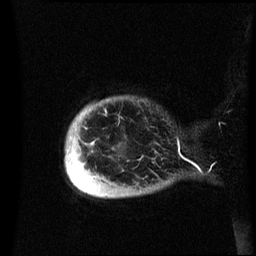
Breast MRI (dynamic contrast-enhanced), one sagittal slice. Position 3 of 60 along the scan axis. Dynamic contrast-enhanced series, image 2 of 3 at this slice position (ordered by acquisition). 1.5 T. TE 4.2 ms, TR 8.4 ms. 2.4 mm slice thickness. 256 × 256 image matrix, field of view 230 × 230 mm. Patient: female, 49 years.
Outlined on this slice (semi-automatic segmentation, software-assisted and operator-edited):
- analysis volume of interest (the breast-tissue region the enhancement analysis was run in; not a lesion): bounding box [x1, y1, x2, y2] px = [65, 97, 172, 198]
- tumour enhancement mask (voxels above the 70 % enhancement threshold inside the analysis volume of interest): [66, 151, 77, 187]